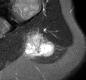
MRI of an extremity soft-tissue mass, one axial slice. STIR. MR volume resampled by the dataset authors to the PET/CT grid (not the native acquisition matrix). 86 × 80 image matrix, field of view 84 × 78 mm. Female patient. From the clinical record (not read from this slice): histological type: malignant fibrous histiocytoma; grade: low; site of the primary tumour: left arm.
Structures marked on this image (expert contour drawn on MRI and transferred to this co-registered scan by the dataset authors):
- gross tumour volume (mass): box from (x=24, y=29) to (x=52, y=57) px